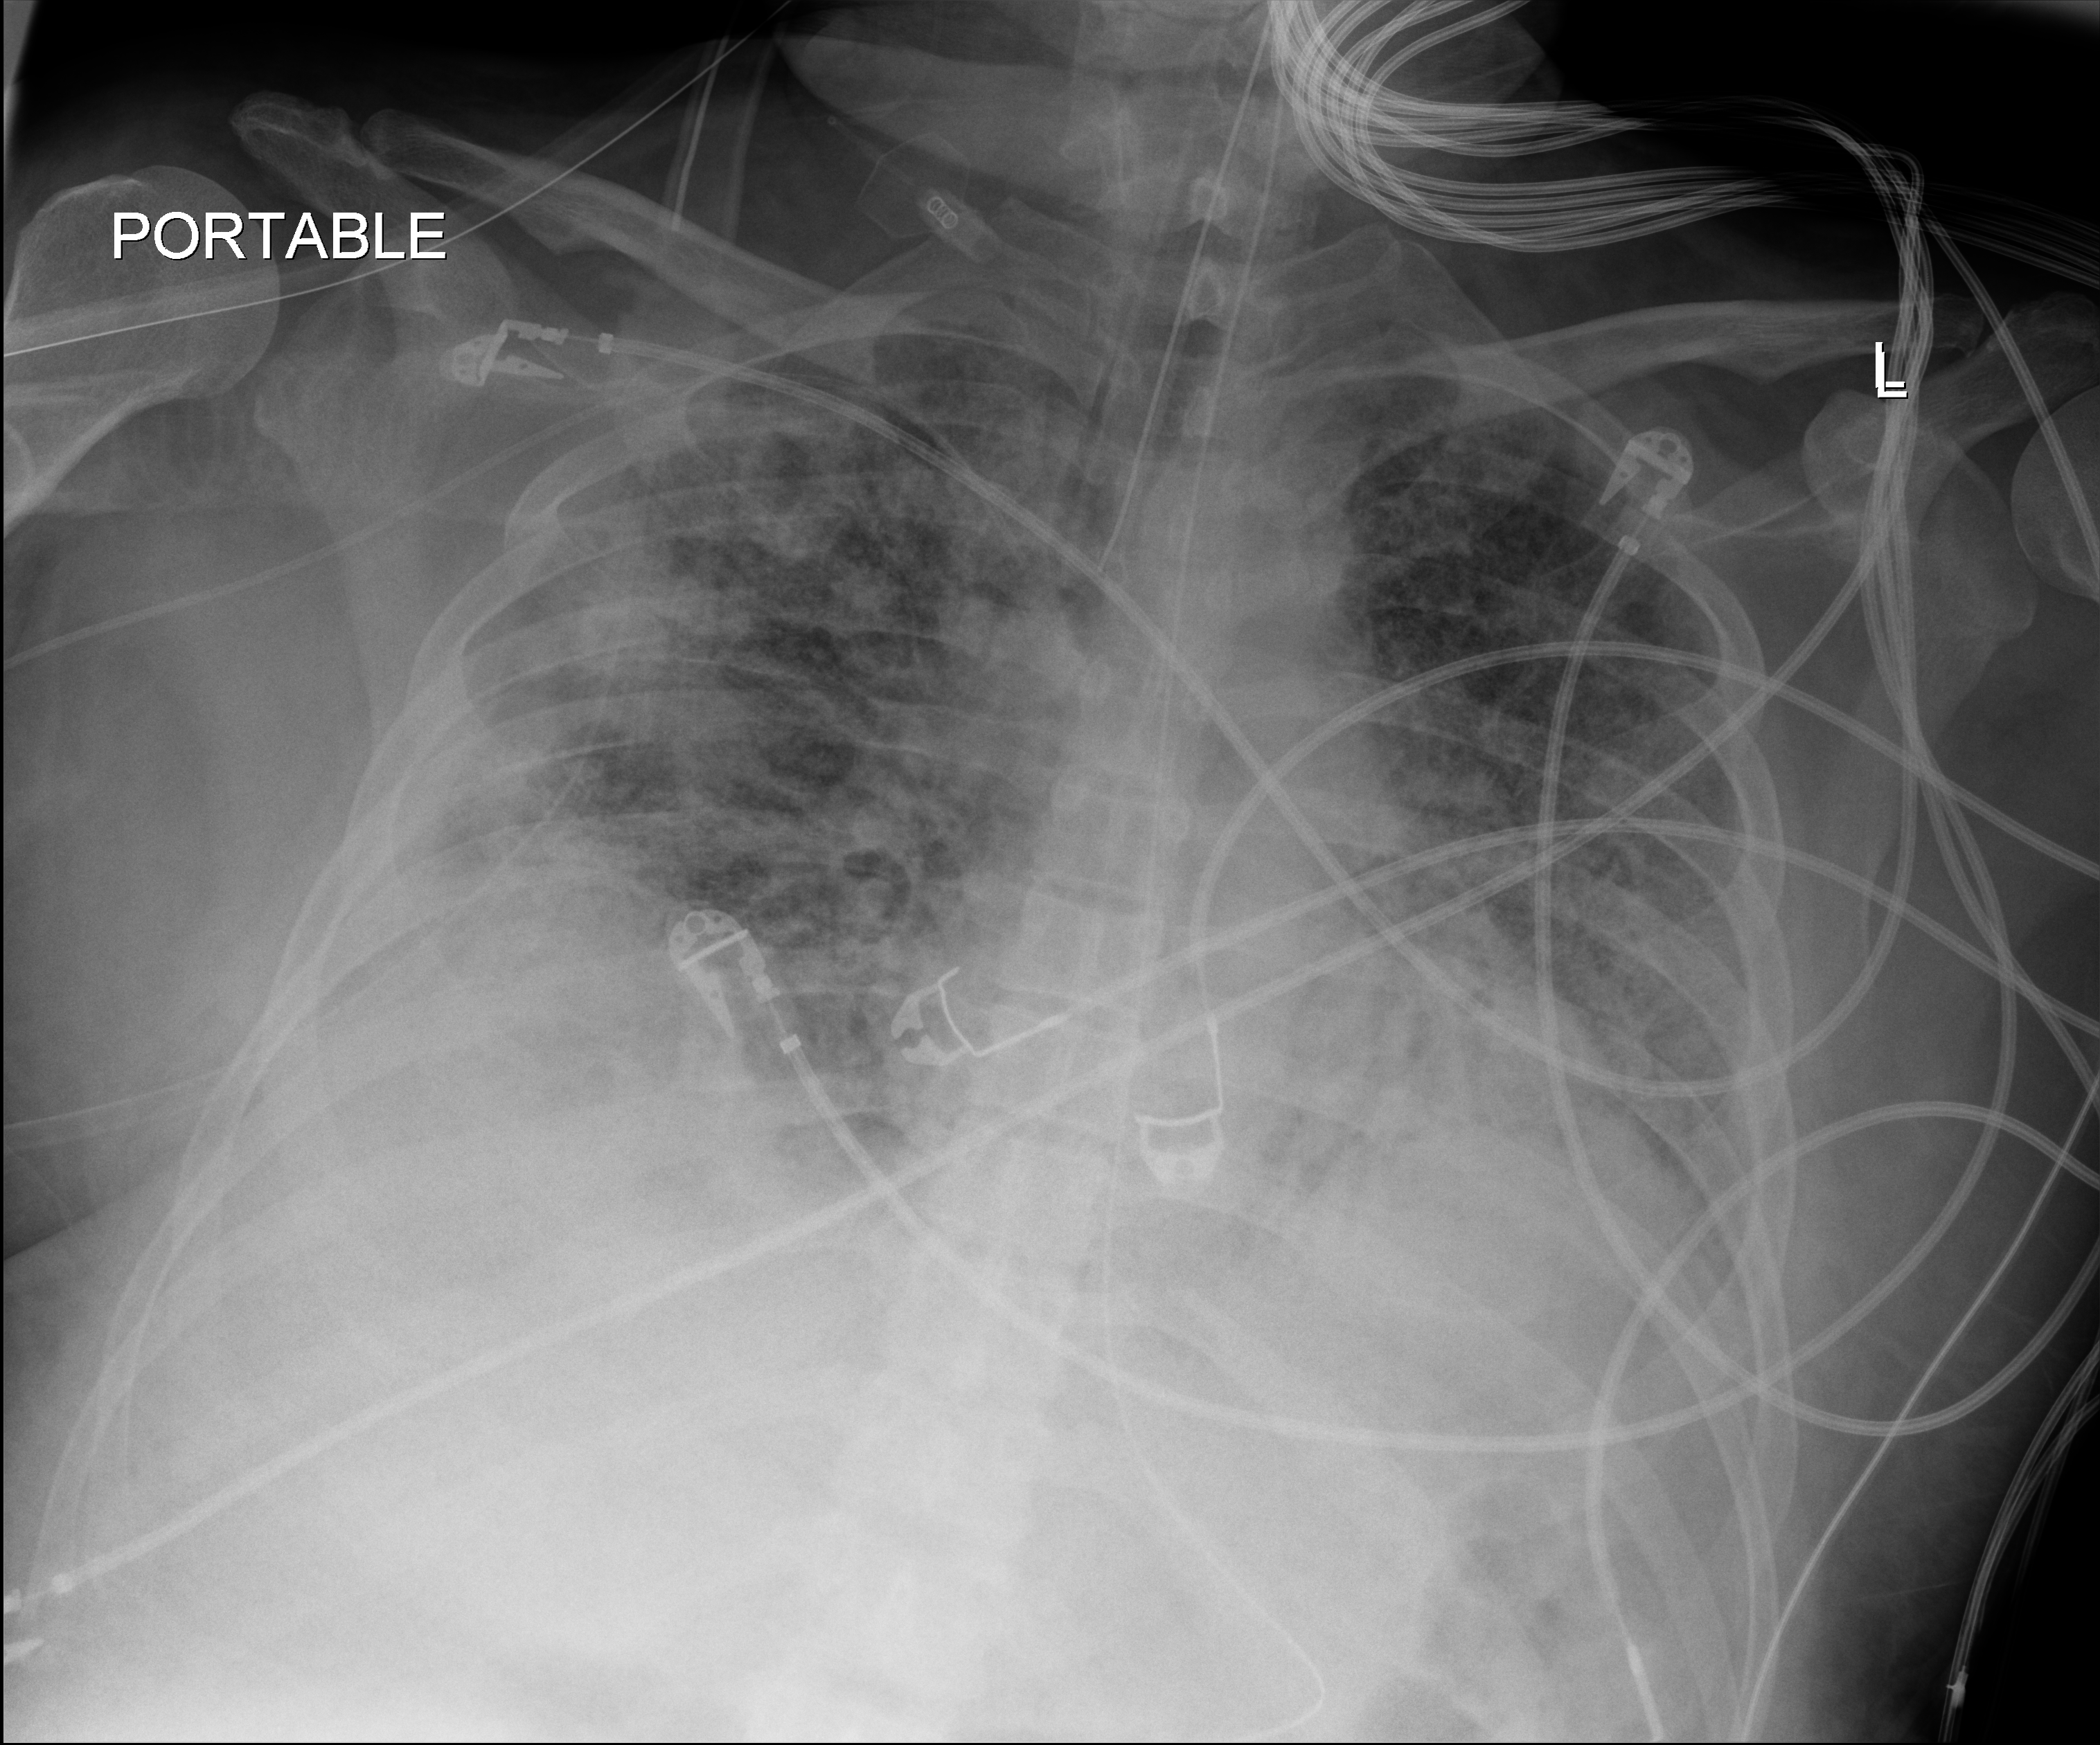
Chest X-ray (portable). Patient hospitalised with COVID-19; male, aged 18–59 years.
Hospital-stay facts (about this admission, not read from this image; timing relative to this image not recorded): other chronic lung disease (admission record): no; admitted to intensive care during this hospital stay: yes.